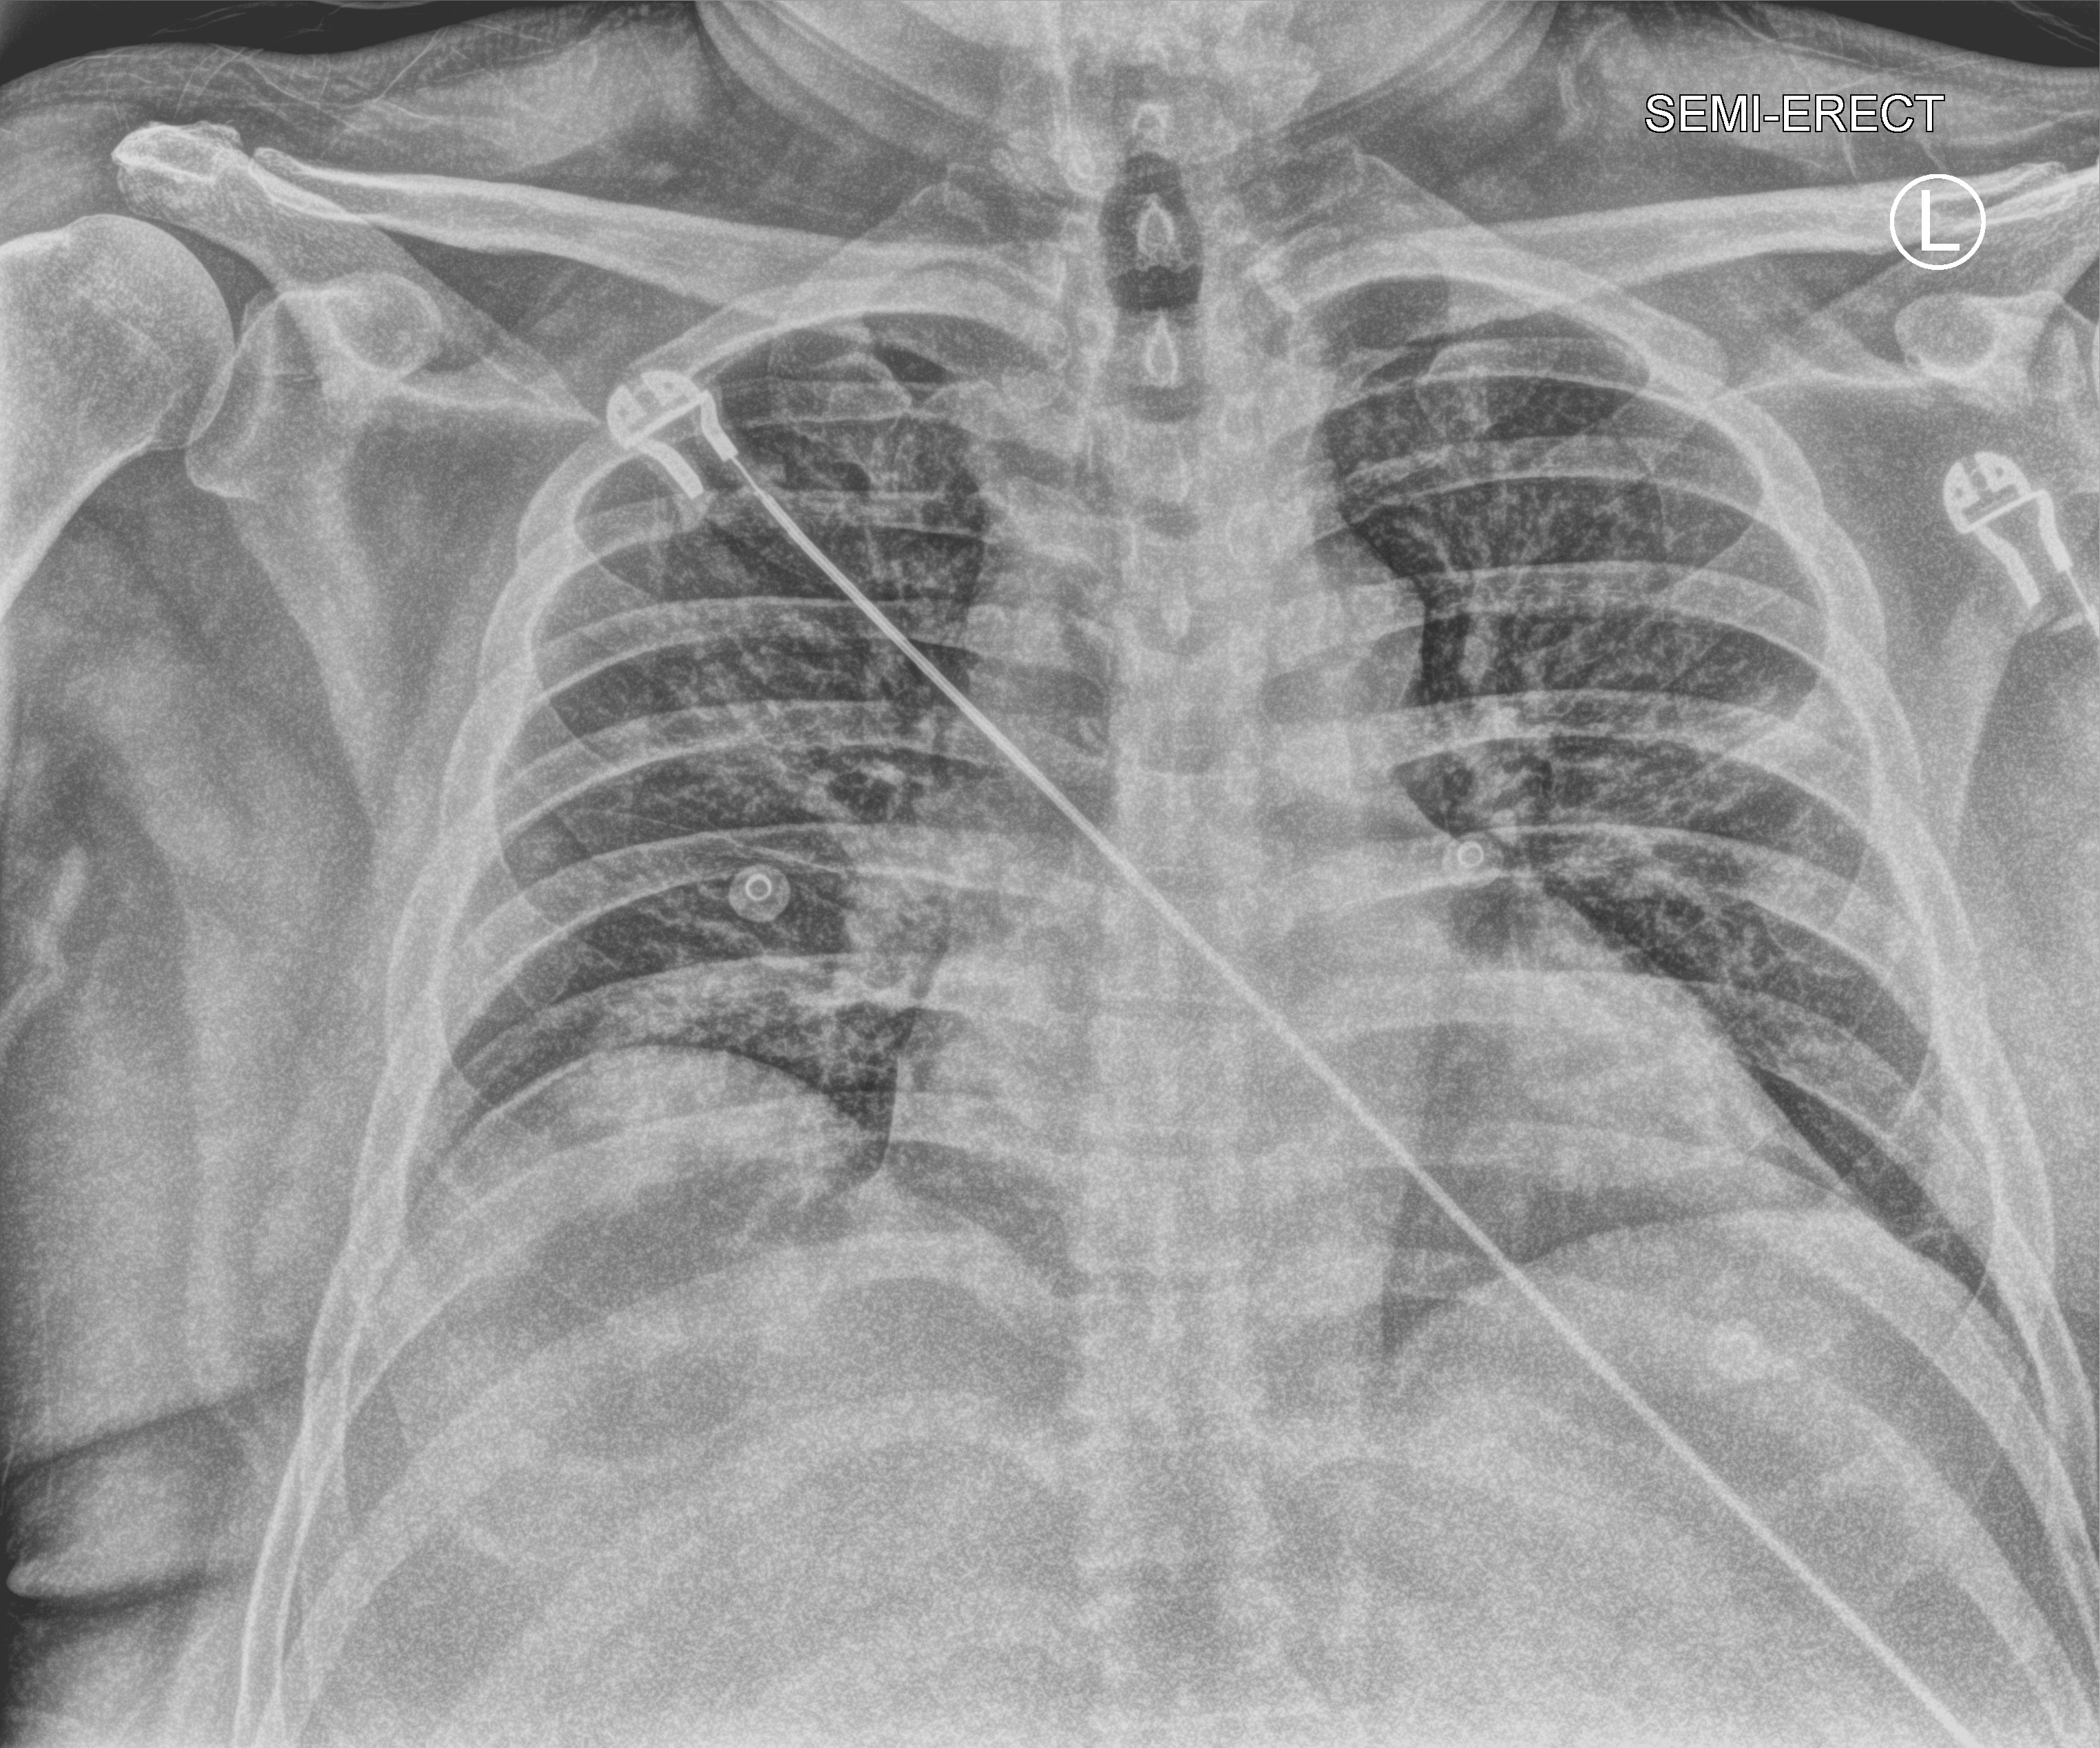
Bedside chest radiograph (computed radiography), anteroposterior (AP) projection. Male patient hospitalised with COVID-19, age 60–74 years.
From the hospital-stay record, not from the radiograph (when in the stay this image was taken is not recorded): admitted to intensive care during this hospital stay: no; mechanically ventilated during this hospital stay: no.